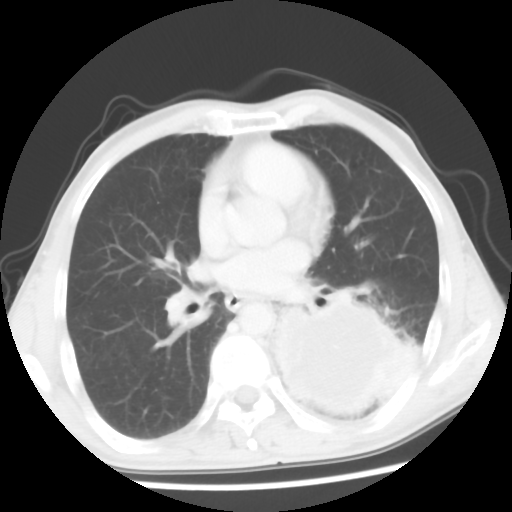
Chest CT, one axial slice; reconstruction kernel STANDARD; 120 kVp; lung window (W 1500 / L -600 HU); 5 mm slice thickness; 512 × 512 image matrix, field of view 318 × 318 mm. Patient: male, 60 years. From the clinical record (not read from this slice): clinical TNM (as recorded): T4 N0 M0.
Outlined on this slice (bounding box drawn by a radiologist):
- lung tumour (recorded histology: squamous cell carcinoma): bounding box (x1, y1, x2, y2) in pixels: (239, 271, 424, 432)